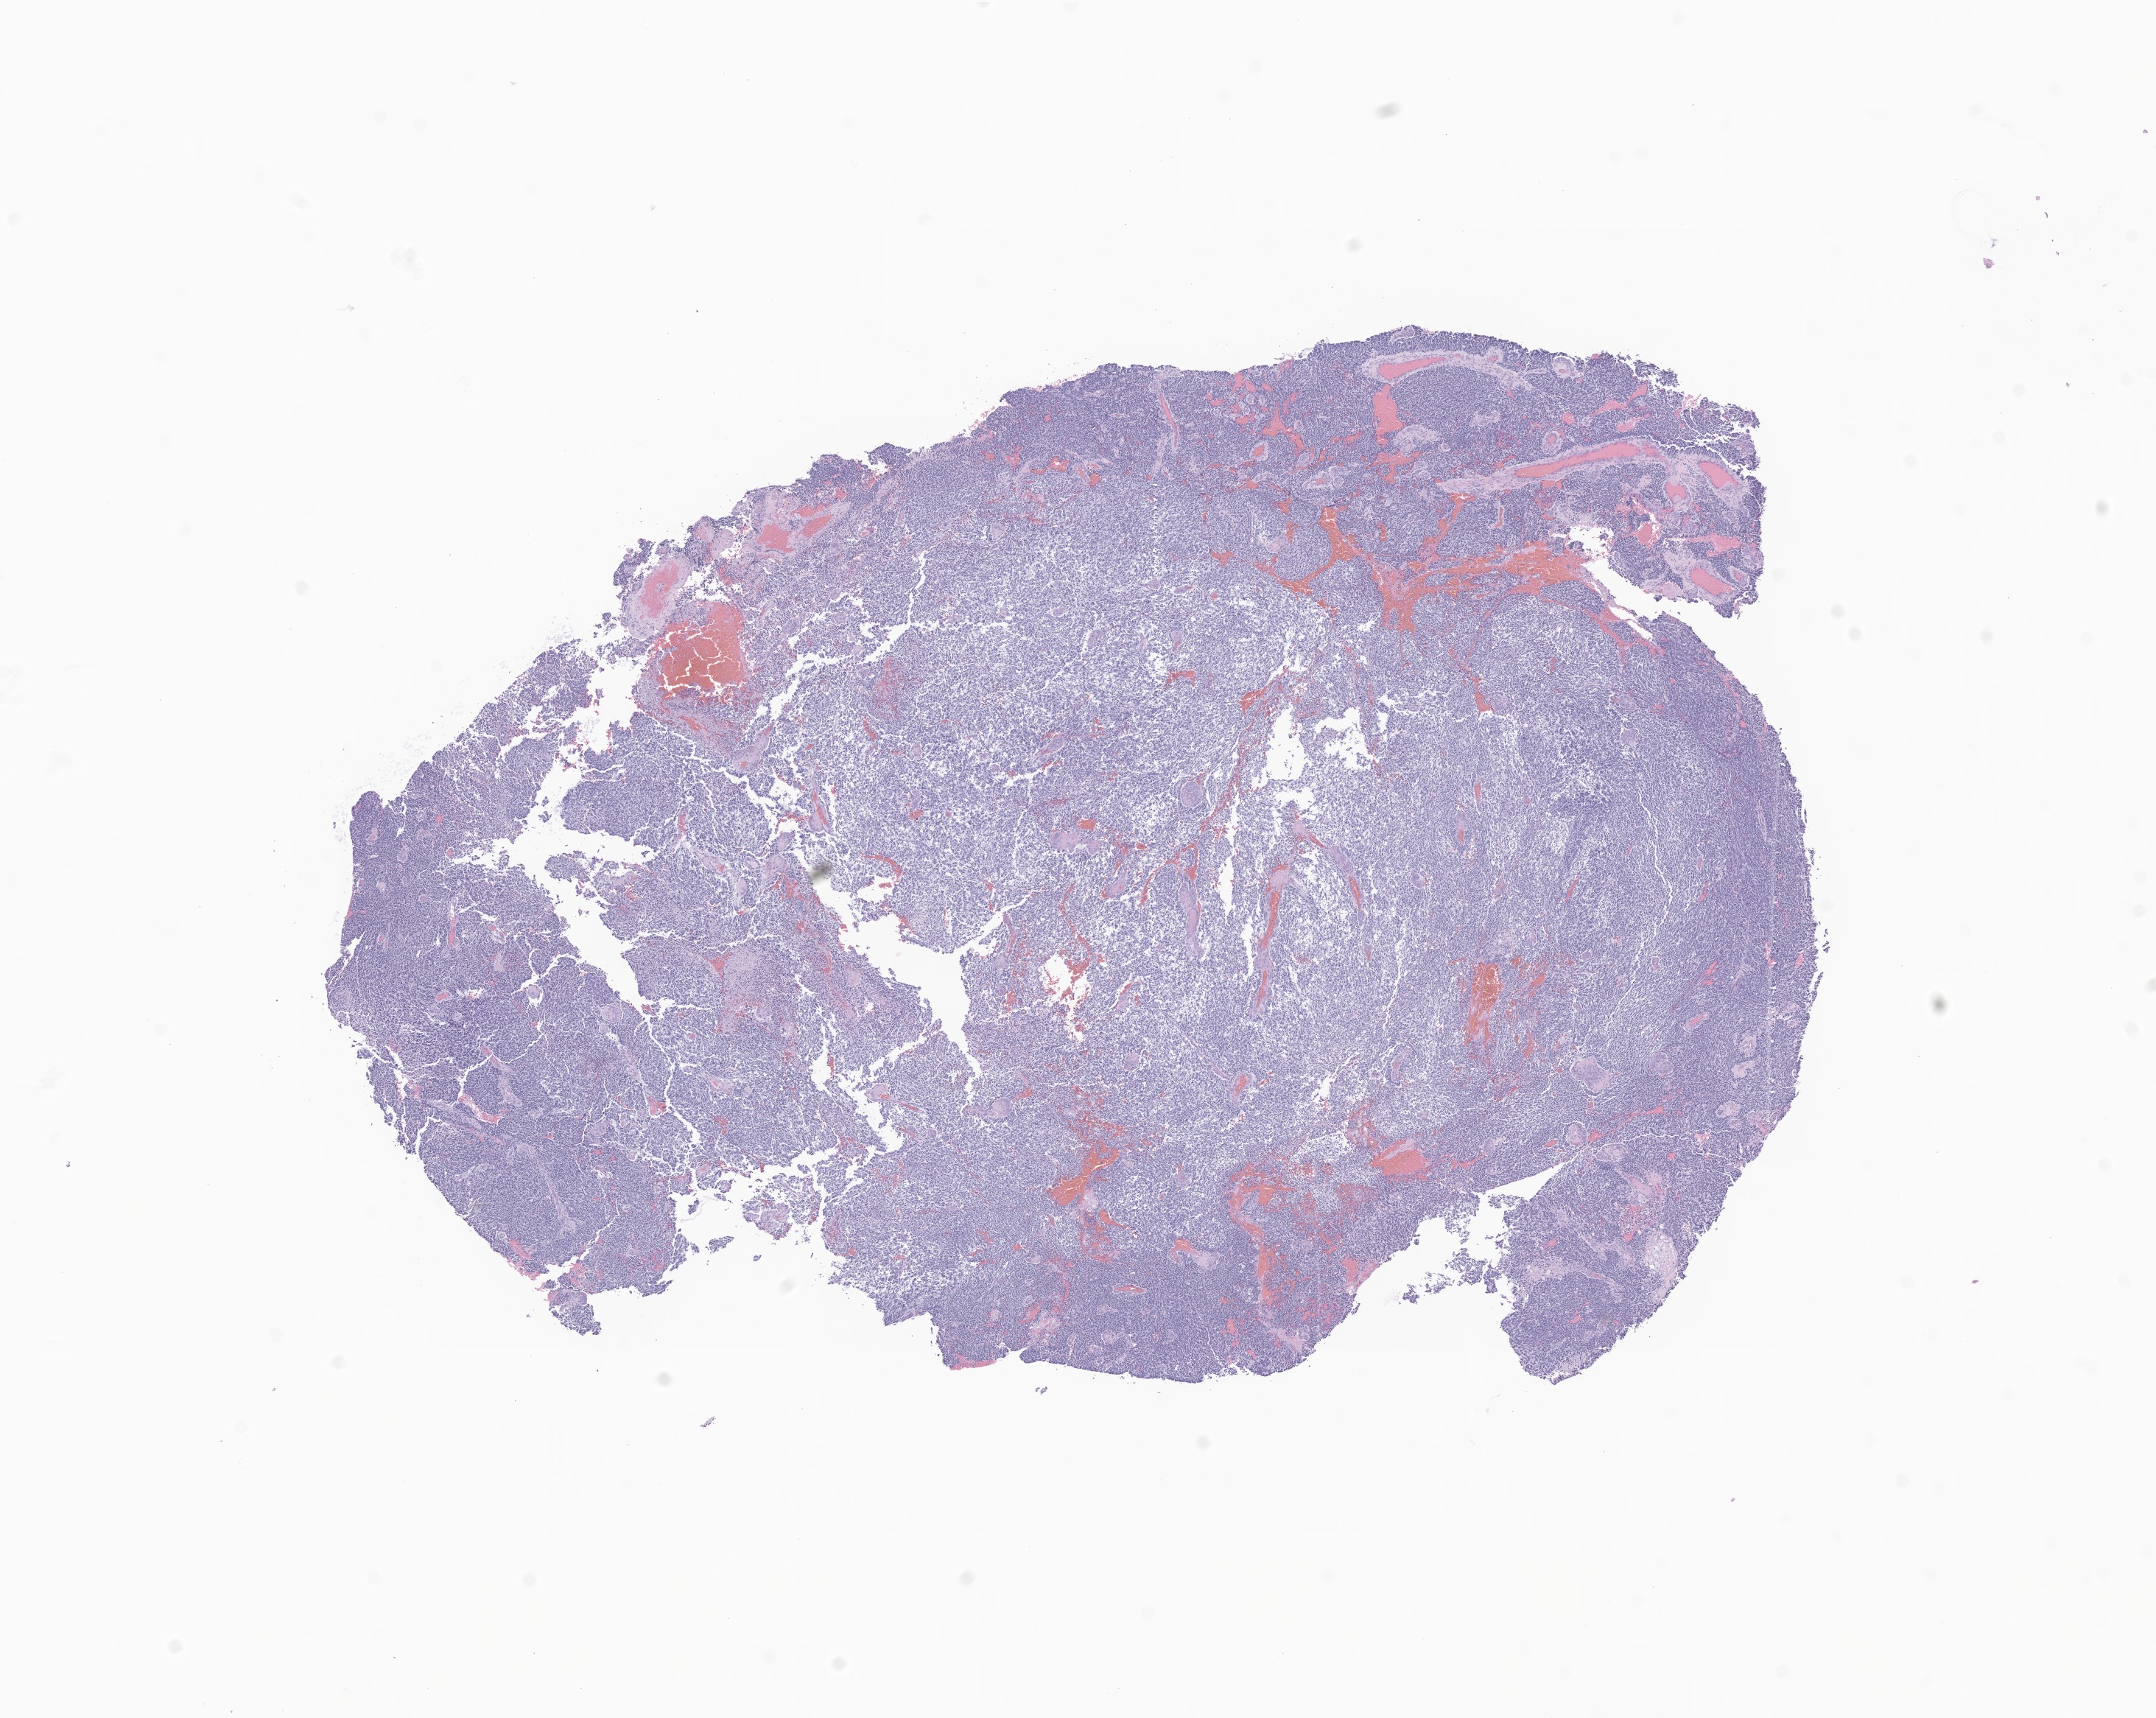
Digitized hematoxylin and eosin (H&E)-stained section of tumor tissue from the brain, shown as a low-resolution overview of the whole scanned area (about 12.3 x 9.8 mm). FFPE section. Patient: female, age 44 months (3 years 8 months).
Recorded diagnosis: Medulloblastoma, NOS.